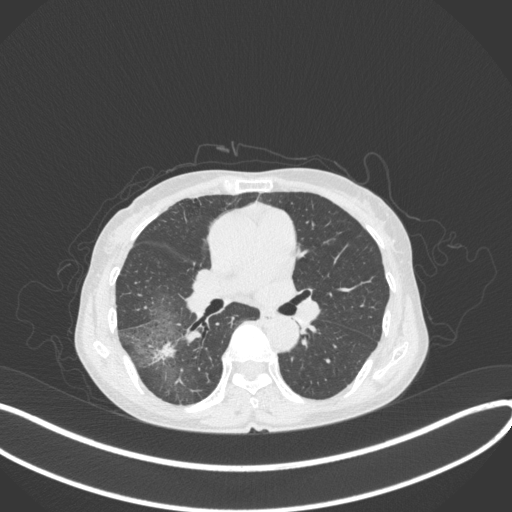
Chest CT, one axial slice; position 218 of 379 along the scan axis; lung window (W 1500 / L -600 HU); 1 mm slice thickness; 512 × 512 image matrix, field of view 400 × 400 mm. Patient: female, 69 years. Case-level facts recorded for this patient, not image findings: clinical TNM (as recorded): T1b N0 M0; histopathological grade: G2-3.
Outlined on this slice (rectangle marked by the reading radiologist):
- lung tumour (recorded histology: adenocarcinoma): box from (x=148, y=336) to (x=178, y=368) px